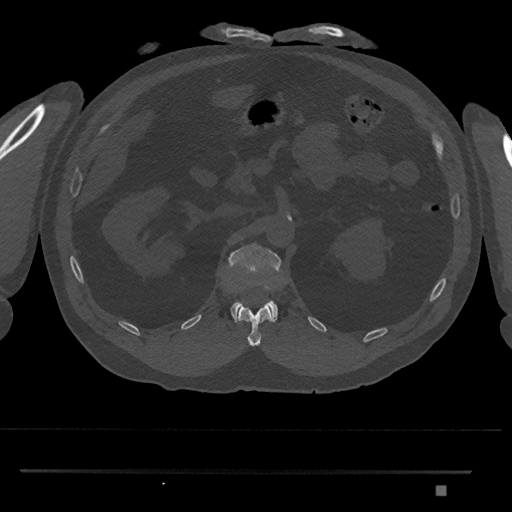
CT including the spine, one axial slice. Slice 857 of 1134 in the series (ordered by position). 120 kVp. Bone window (W 1800 / L 400 HU). 512 × 512 image matrix. Patient: male, 65 years. From the clinical record (not read from this slice): primary cancer: prostate.
Structures marked on this image (semi-automatic segmentation, software-assisted and operator-edited):
- L1 vertebra: bounding box [x1, y1, x2, y2] px = [228, 243, 281, 322]
- T12 vertebra: [237, 304, 272, 346]